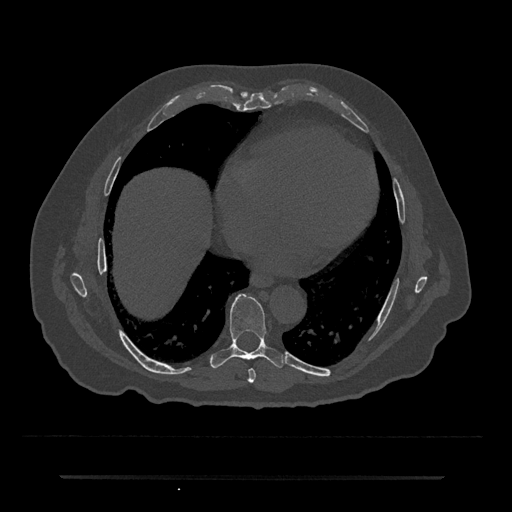
CT including the spine, one axial slice. Position 338 of 797 along the scan axis. 120 kVp. Bone window (W 1800 / L 400 HU). 0.5 mm slice thickness. 512 × 512 image matrix, field of view 437 × 437 mm. Male patient, age 69 years. Case-level facts recorded for this patient, not image findings: primary cancer: prostate.
Outlined on this slice (semi-automatically segmented with operator editing):
- T7 vertebra: bounding box [x1, y1, x2, y2] px = [248, 368, 256, 383]
- T8 vertebra: [211, 293, 284, 368]